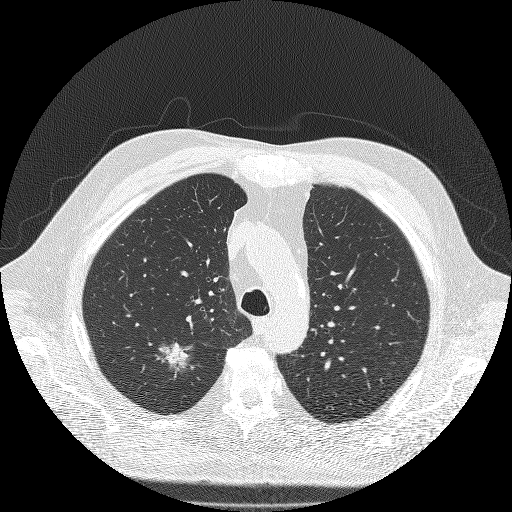
Low-dose screening chest CT, axial slice; second annual screen; lung window (W 1500 / L -600 HU); 2 mm slice thickness; lung (sharp) reconstruction kernel (FC51); 120 kVp; slice 36 of 180 in the series; 512 × 512 image matrix, field of view 385 × 385 mm. Male, age 71 years at enrolment. Former smoker at enrolment.
Expert reader's lesion annotation, bounding box (x1, y1, x2, y2) in pixels: (138, 326, 205, 389). The screening reader recorded 3 non-calcified nodules or masses ≥4 mm on this exam (right upper lobe, right upper lobe, right lower lobe); which of them this box marks is not recorded. Participant outcome: lung cancer diagnosed 59 days after this screen — bronchiolo-alveolar adenocarcinoma, NOS, right upper lobe, moderately differentiated (G2), stage IIIA (AJCC 6th edition), 25 mm at pathology.